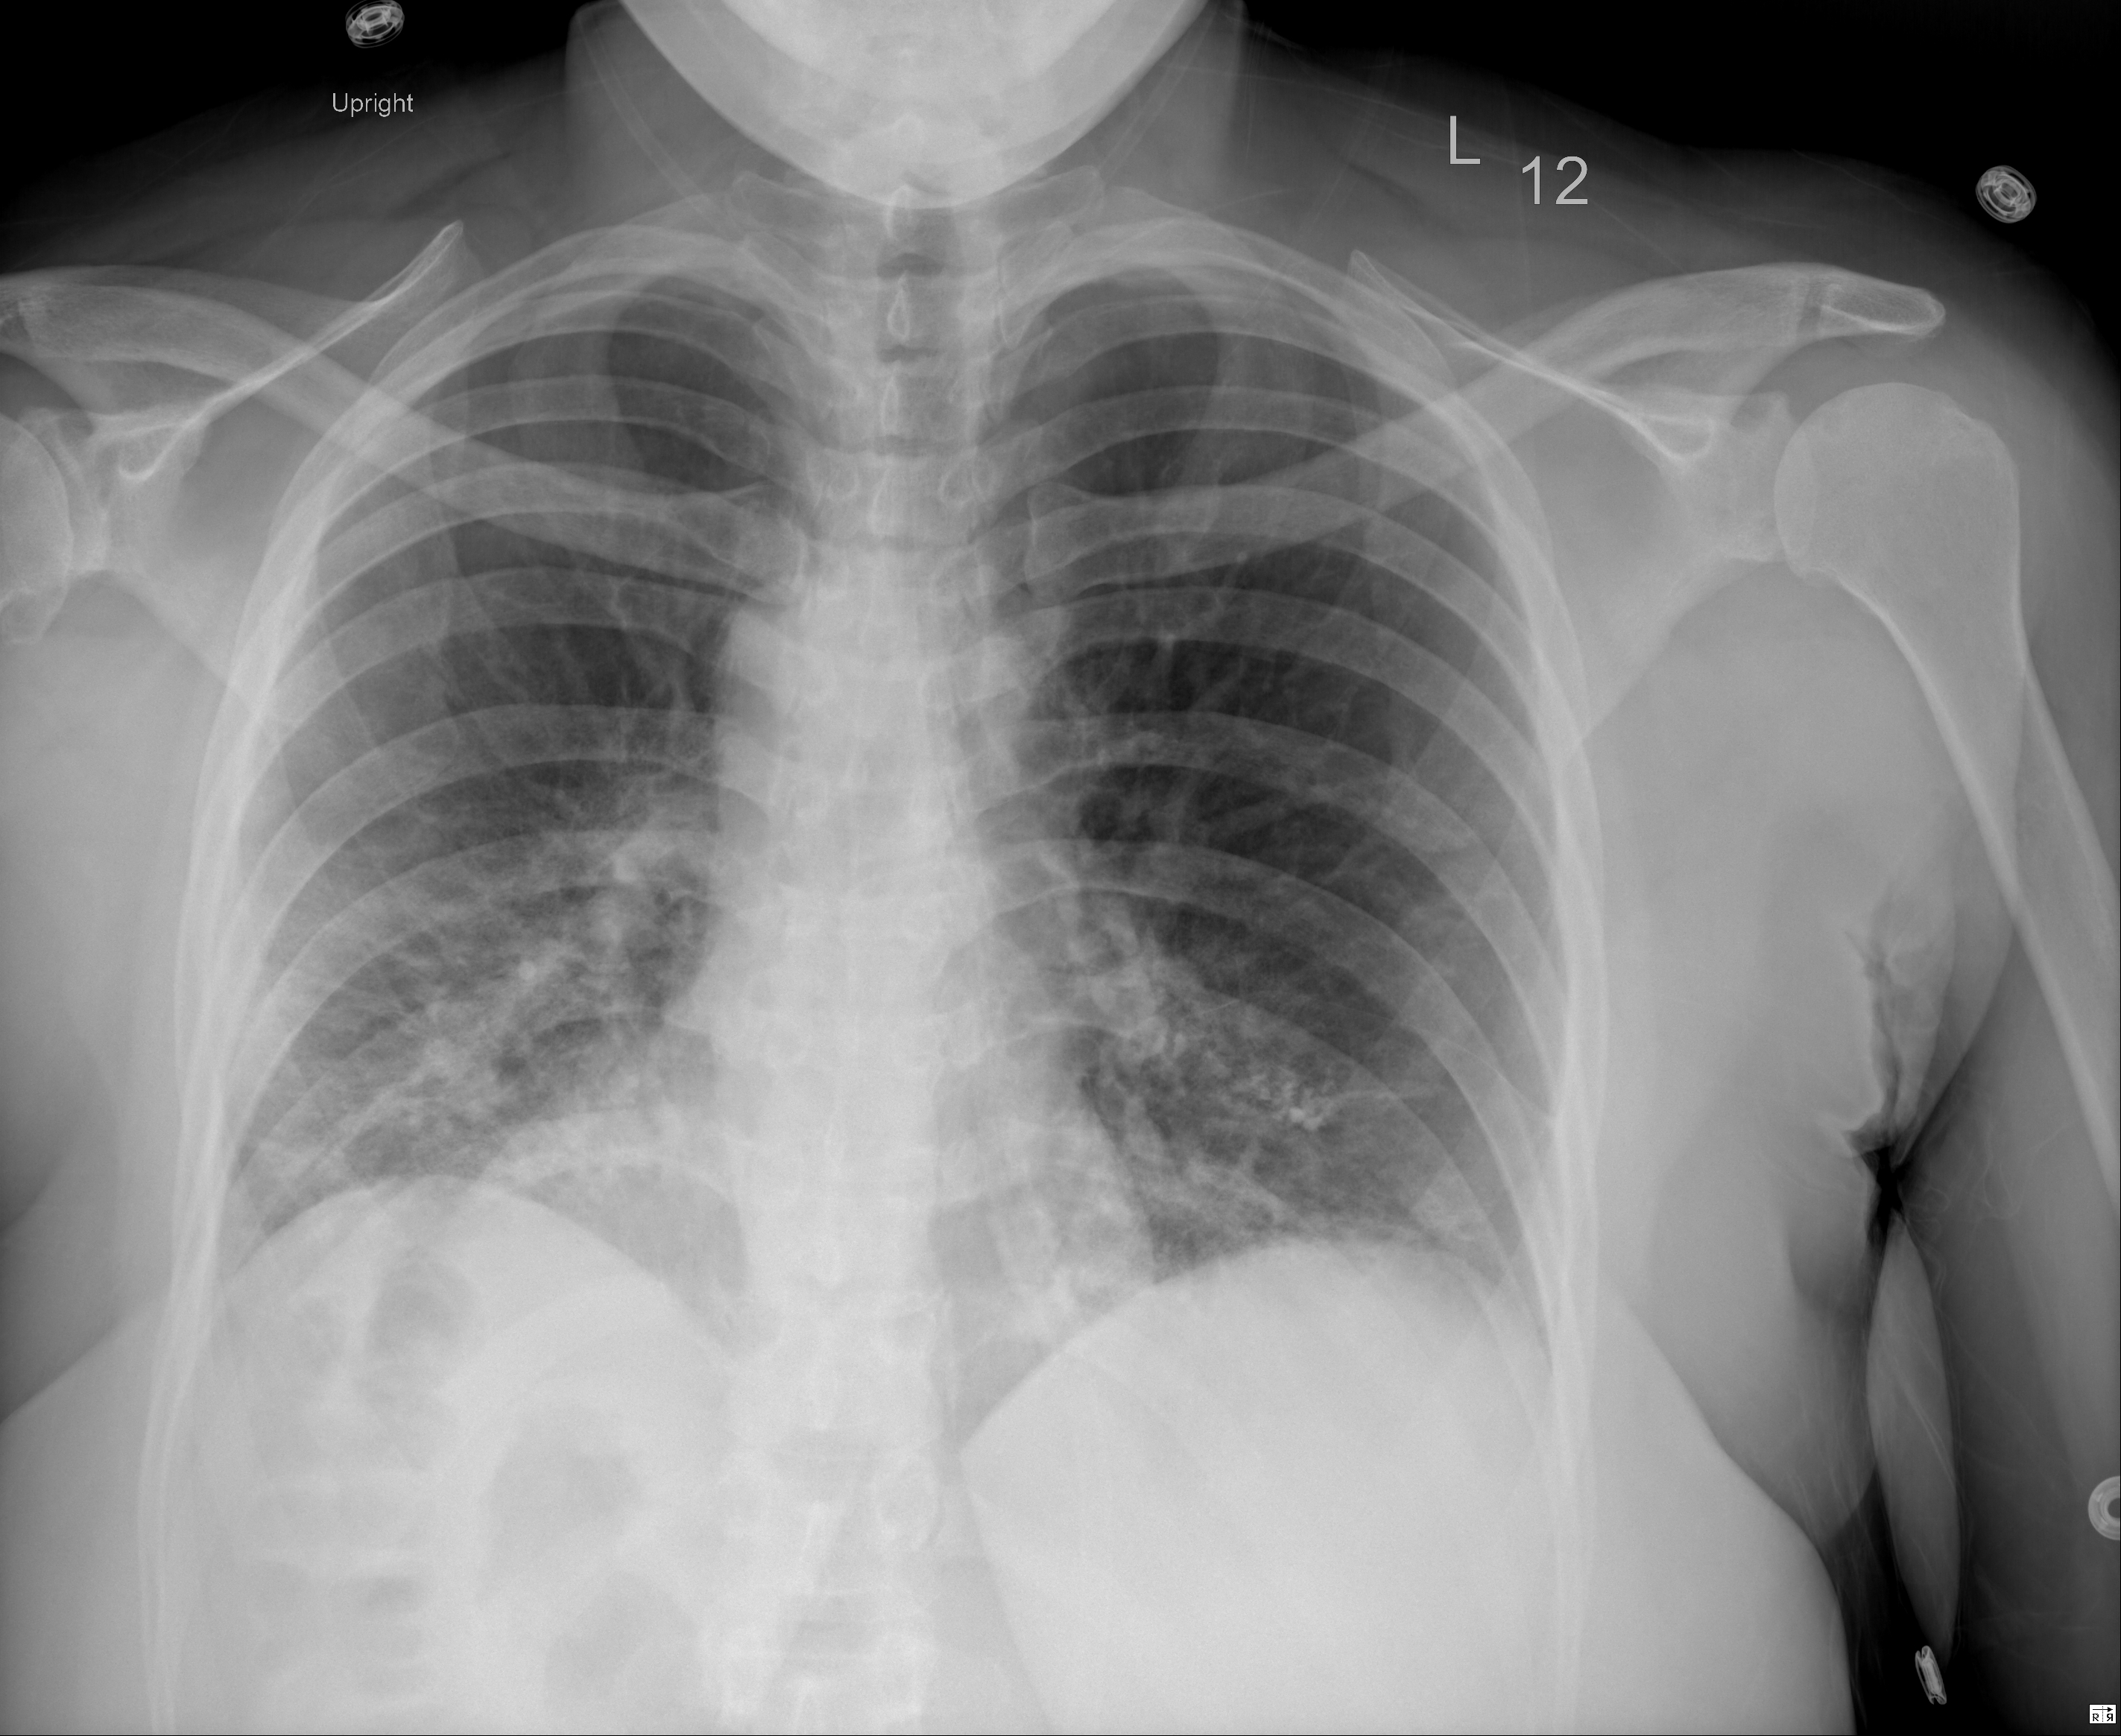
Chest X-ray, PA projection. Female patient, age 58 years; imaged 2 days after the COVID-19 diagnosis.
Radiologist key findings (as recorded): Persistent bibasilar opacity consistent somewhat worse on left than right, overall very little change.